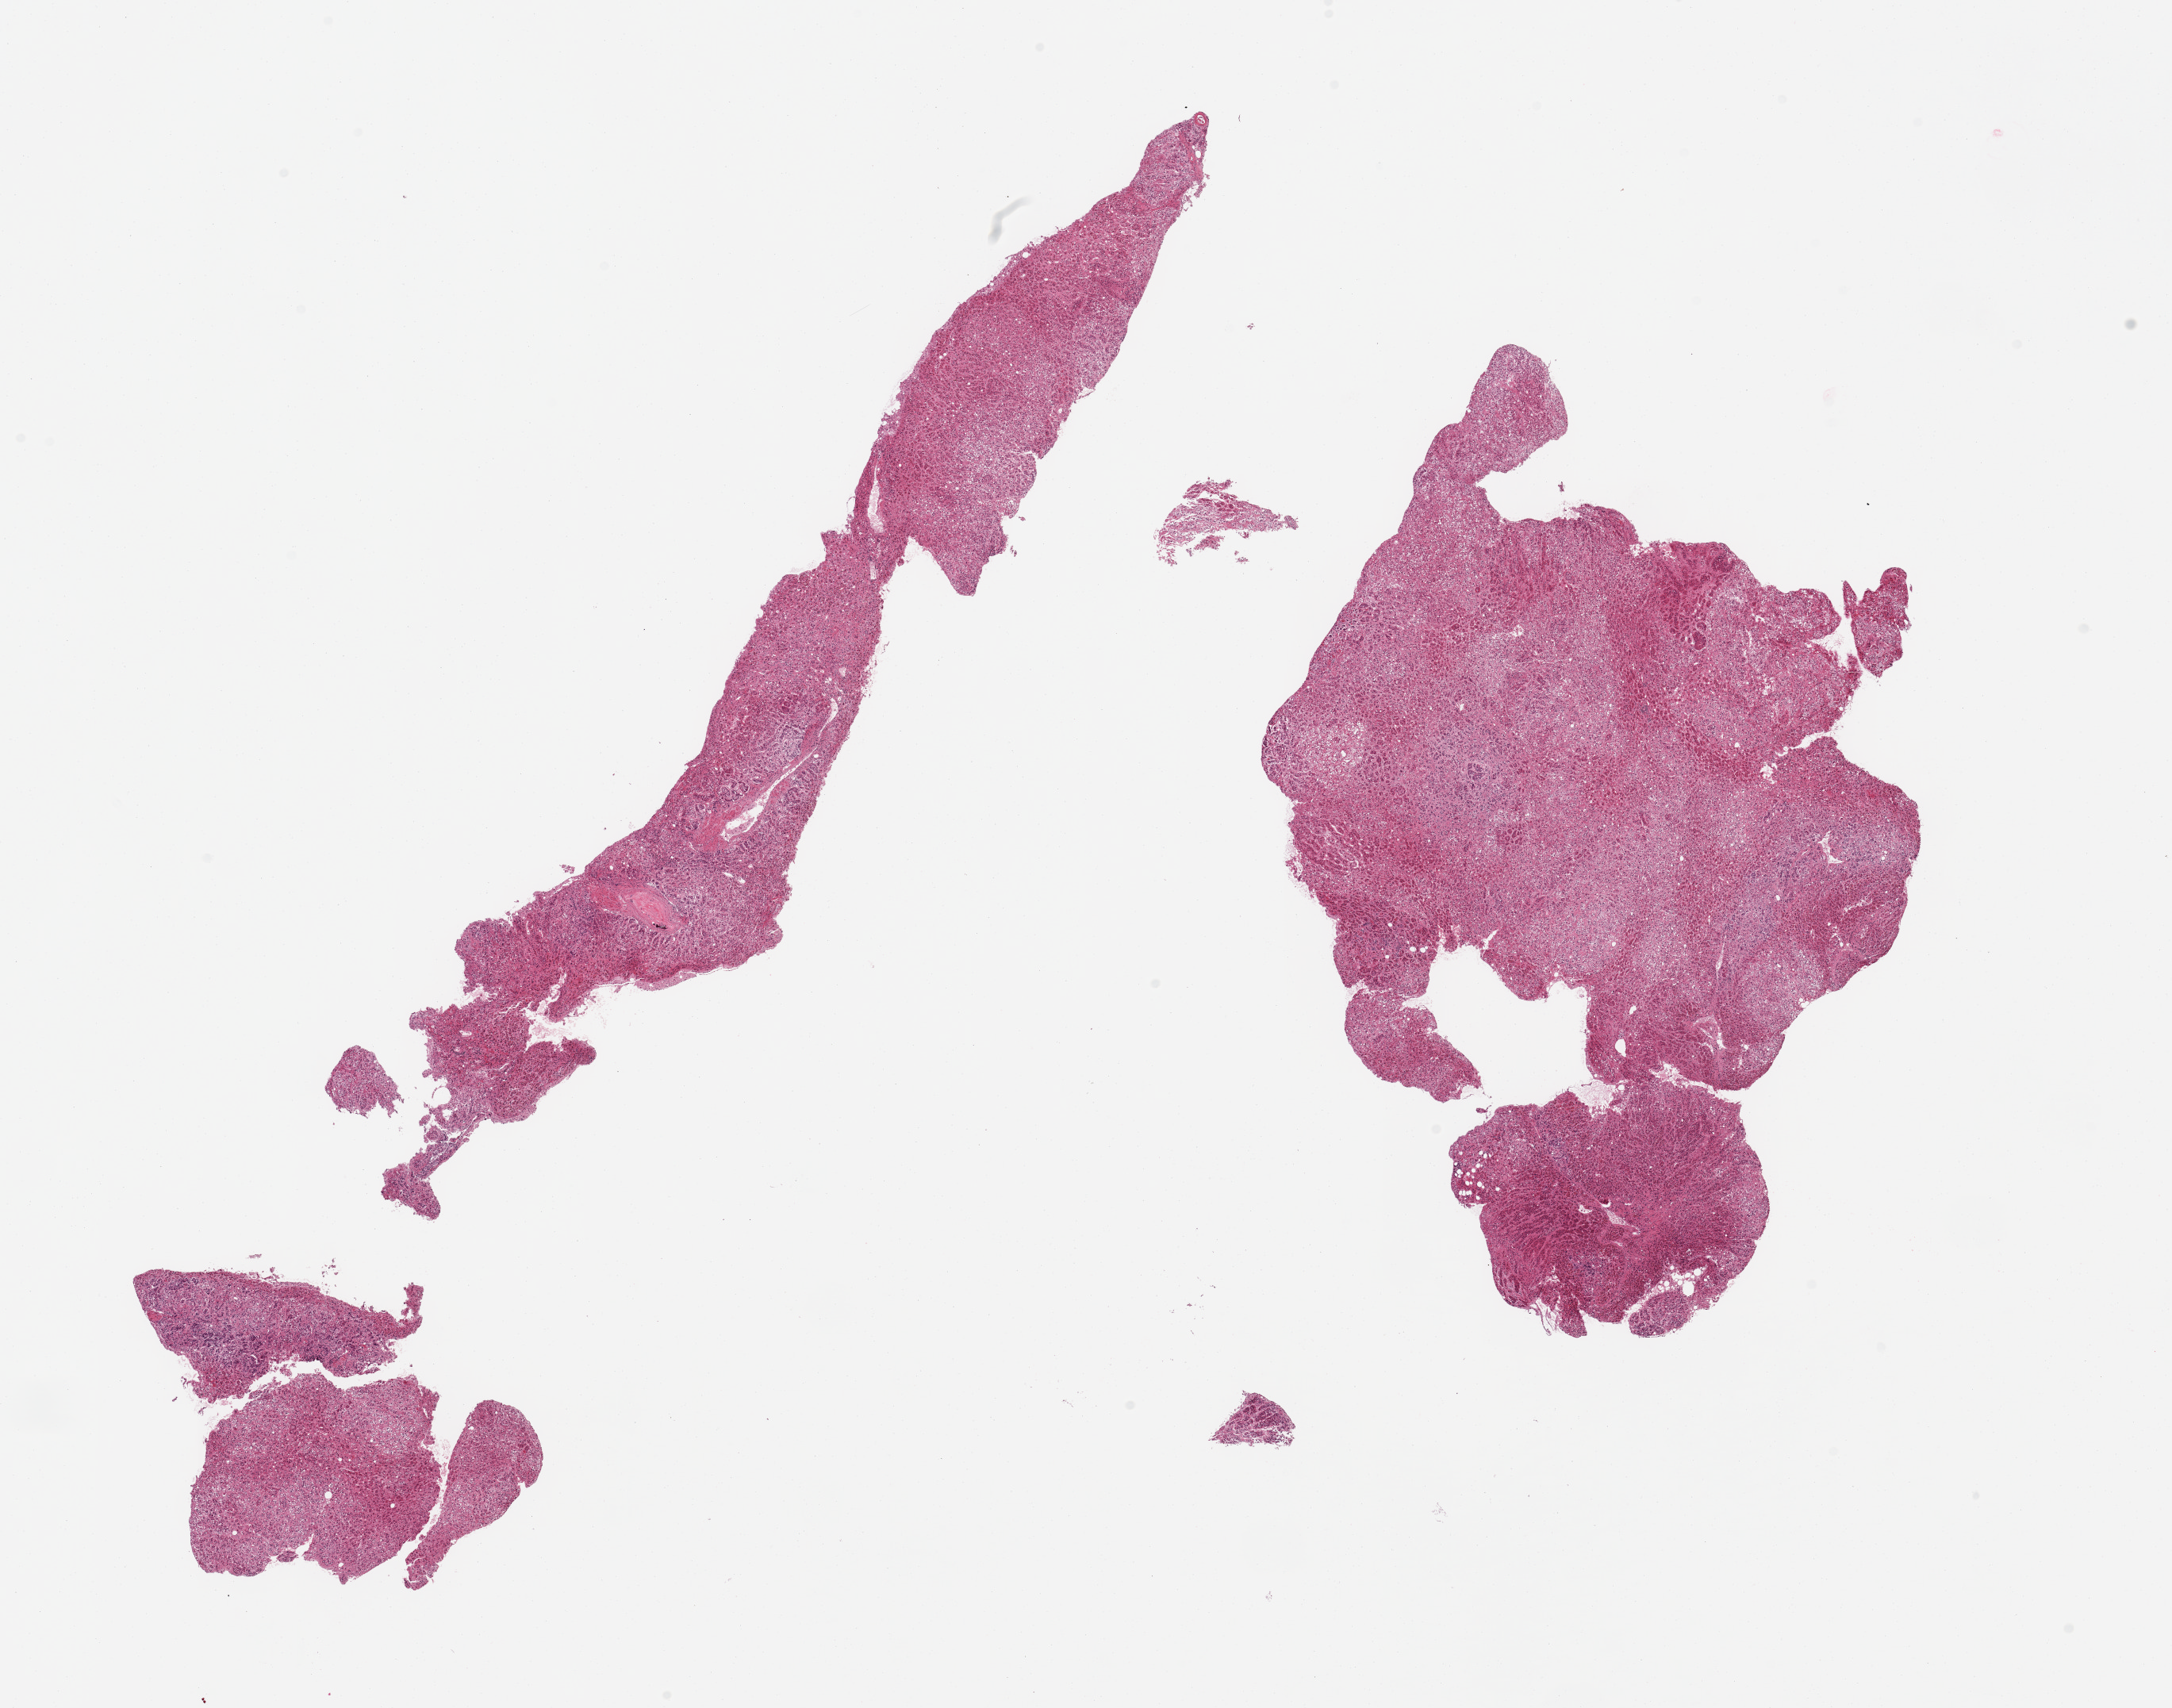
Whole-slide image, haematoxylin and eosin stain, whole scanned area (about 21.7 x 17.0 mm, slide scanned at 20x) shown as a low-resolution overview; PAXgene-fixed, paraffin-embedded tissue; target tissue: adrenal gland; tissue donor sample. Female donor.
Pathologist's review note for this sample: 2 pieces; fragmented, predominantly adrenal cortex.